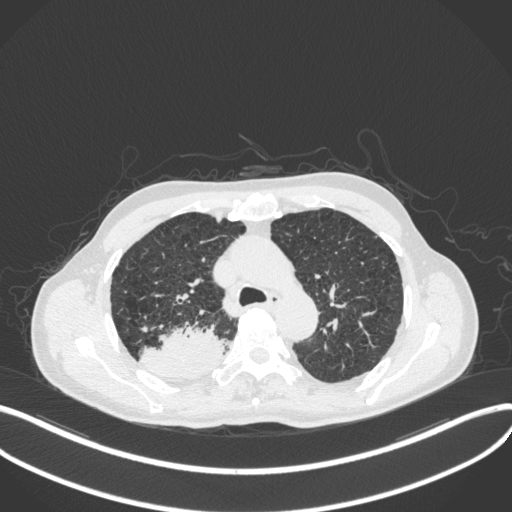
Chest CT, one axial slice. Slice 321 of 423 in the series (ordered by position). Reconstruction kernel B31f. 120 kVp. Lung window (W 1500 / L -600 HU). 512 × 512 image matrix. Patient: male, 79 years. Case-level facts recorded for this patient, not image findings: clinical TNM (as recorded): T3 N0 M0.
Annotated regions visible in this slice (rectangle marked by the reading radiologist):
- lung tumour (recorded histology: adenocarcinoma): box from (x=138, y=320) to (x=226, y=380) px